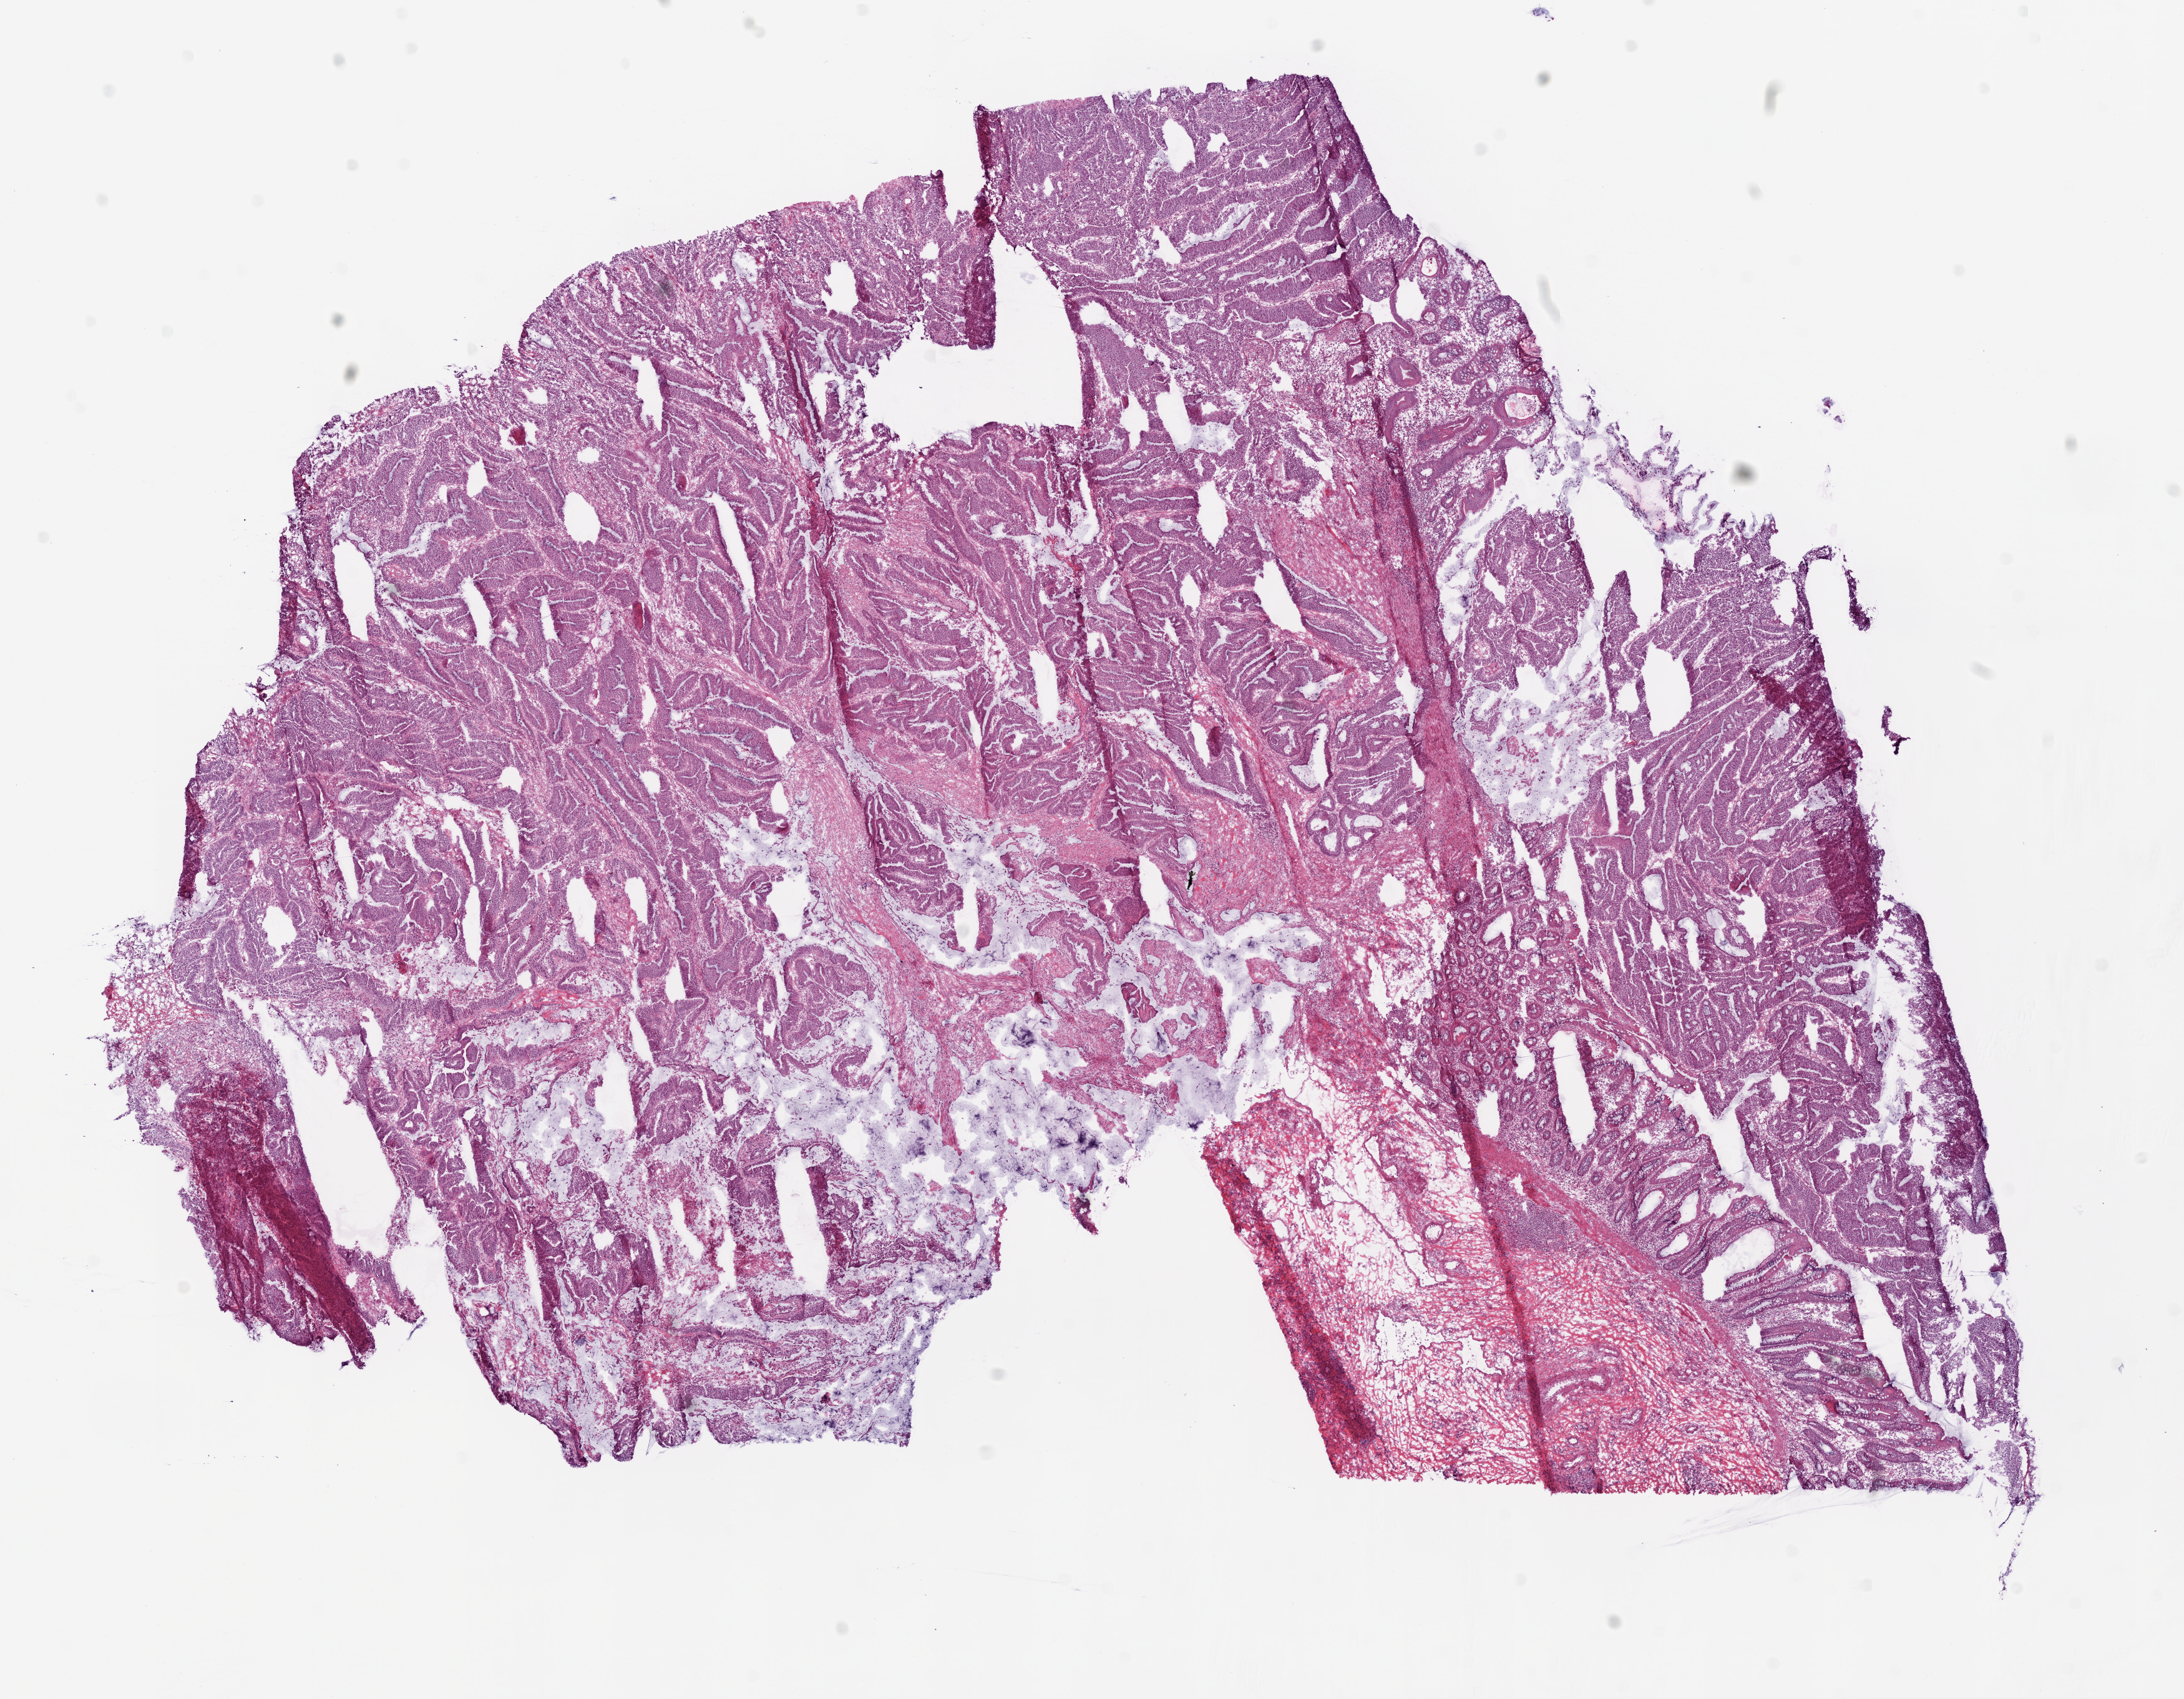
Whole-slide histology image, Hematoxylin and eosin (H&E) stained — shown as a low-resolution overview of the whole scanned area (about 14.0 x 10.9 mm, from a 20x scan). Frozen section from the top of the tissue portion. Colon, primary tumour sample. Male patient; age at initial diagnosis 71 years. Composition of this section per pathologist review: tumour cells 80%, tumour nuclei 85%, normal cells 5%, stromal cells 10%, necrosis 5%.
AJCC pathologic stage: II (5th edition). Diagnosis: Adenocarcinoma, NOS (cecum). TNM: T3 N0 M0.